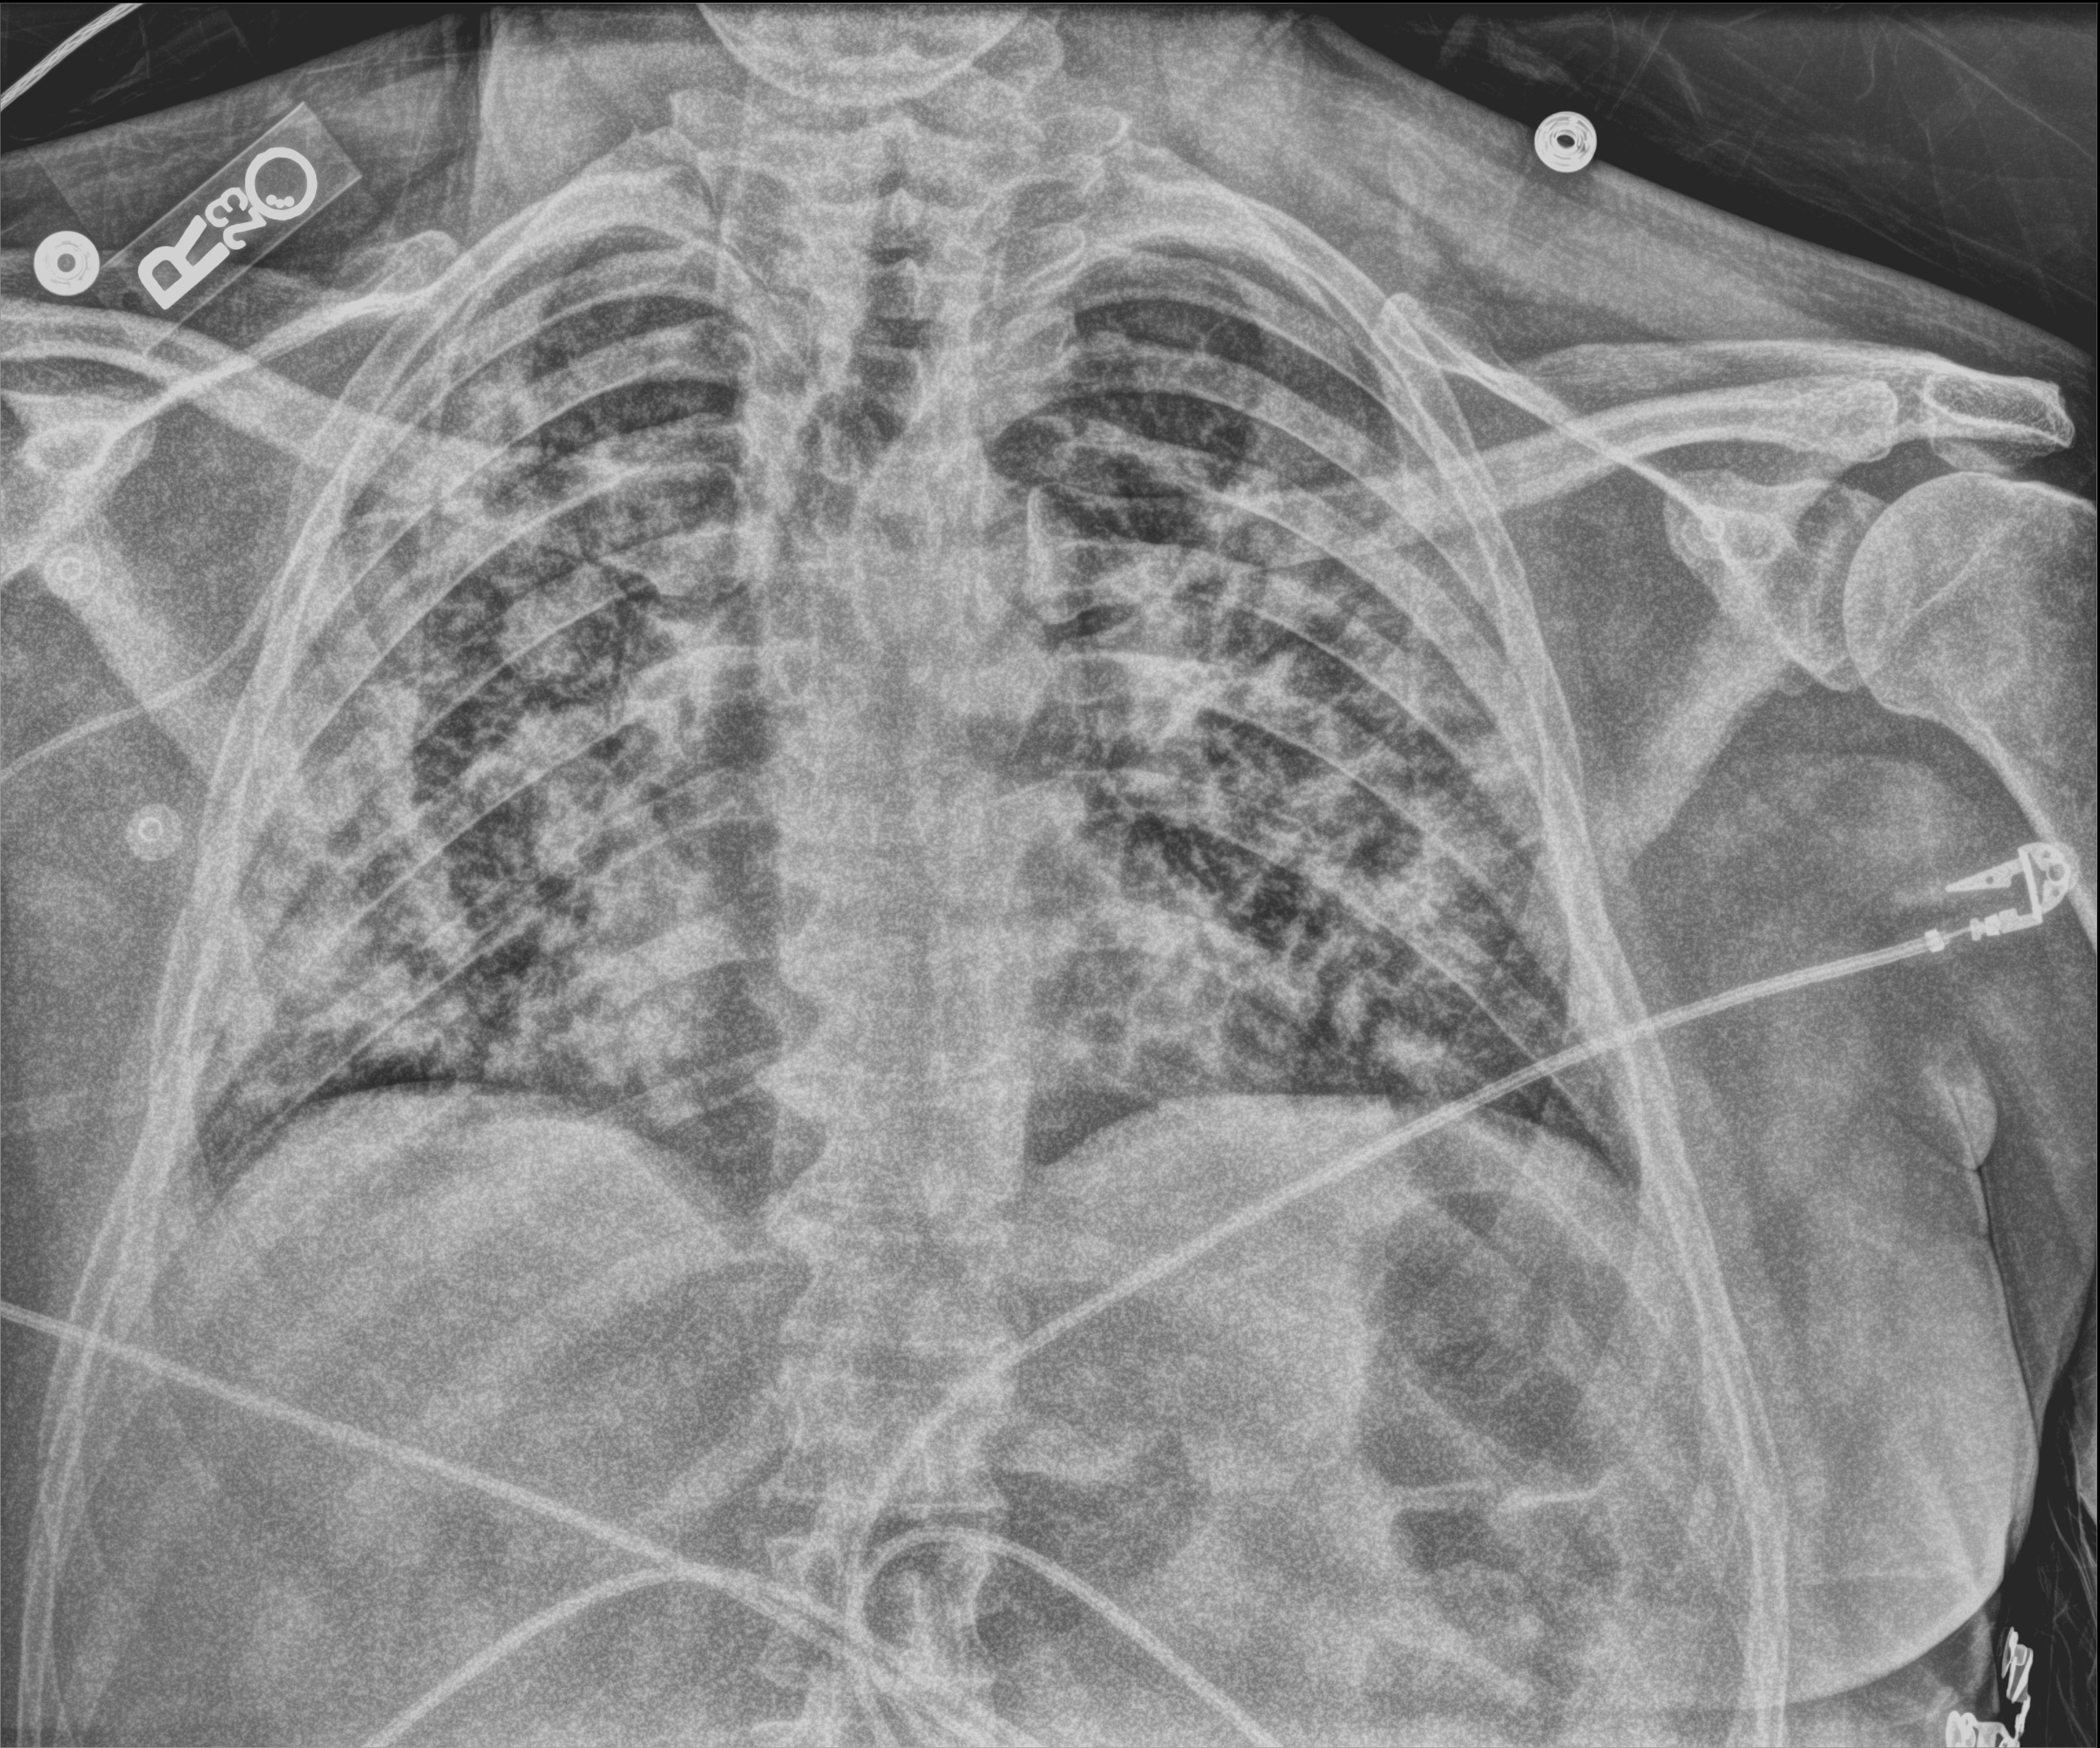
Chest X-ray (portable), anteroposterior (AP) projection. Male patient hospitalised with COVID-19, age 18–59 years.
From the hospital-stay record, not from the radiograph (when in the stay this image was taken is not recorded):
- mechanically ventilated during this hospital stay: no
- admitted to intensive care during this hospital stay: yes
- diabetes (admission record): no